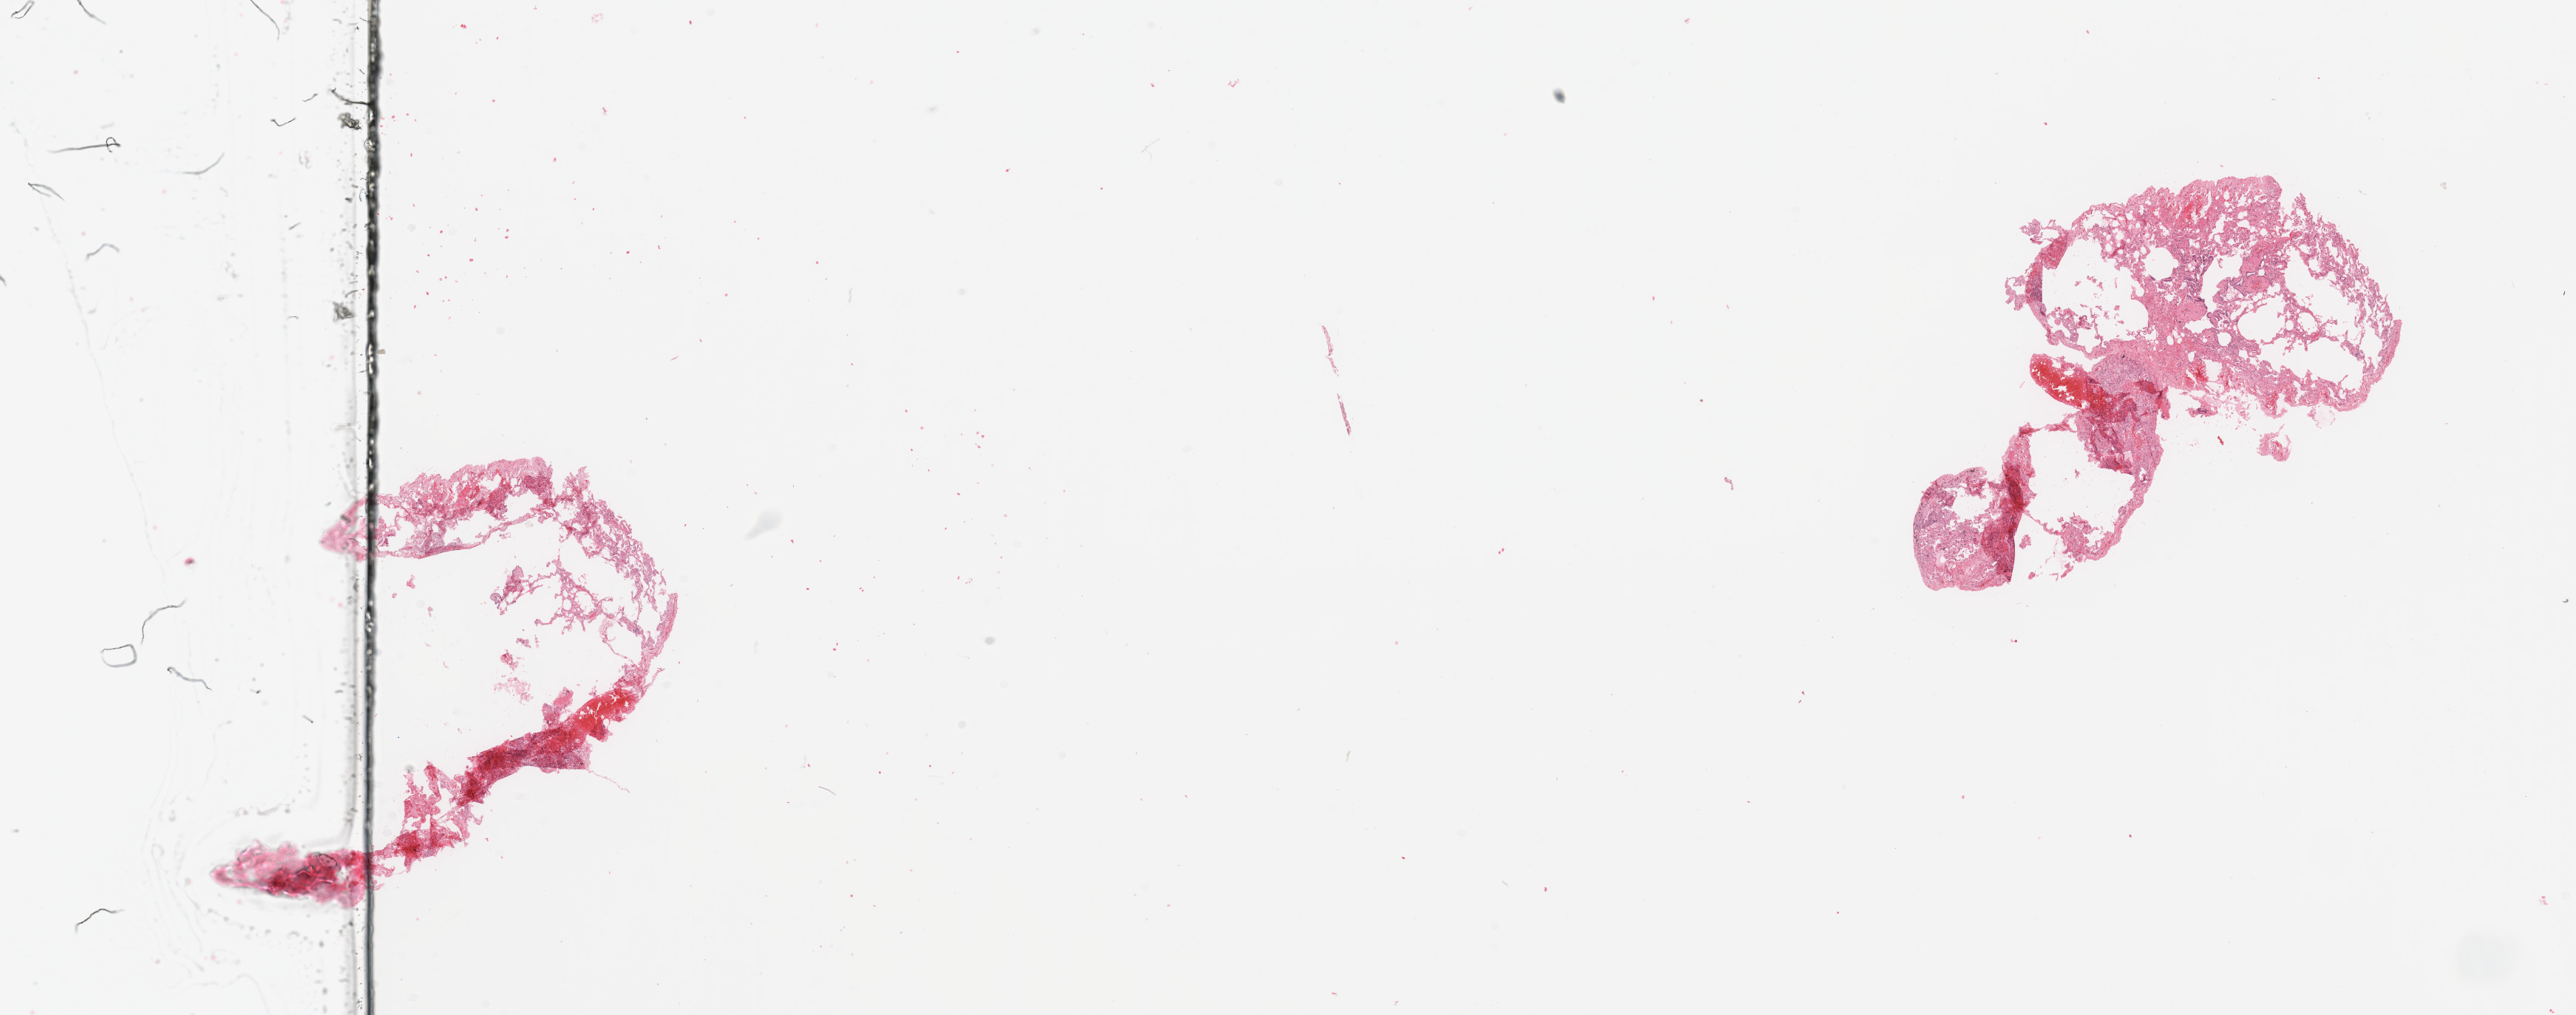
Hematoxylin and eosin (H&E) stained whole-slide image — shown as a low-resolution overview of the whole scanned area (about 27.6 x 10.9 mm, slide scanned at 20x), normal (non-tumour) tissue sample, lung. 78-year-old female patient.
- this section: normal (non-tumour) tissue from the same patient
- patient diagnosis: Adenocarcinoma, NOS